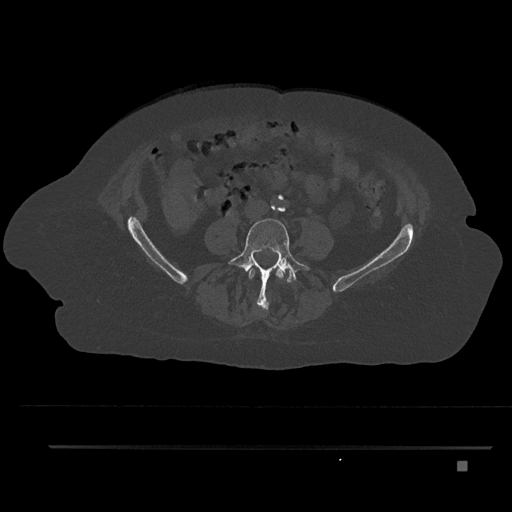
CT including the spine, one axial slice; slice 84 of 797 in the series (ordered by position); reconstruction kernel Br40s/3; 120 kVp; bone window (W 1800 / L 400 HU); 0.5 mm slice thickness; 512 × 512 image matrix, field of view 437 × 437 mm. Patient: female, 76 years. Case-level facts recorded for this patient, not image findings: primary cancer: lung; vertebrae with lytic lesions (as recorded): T11, L3.
Structures marked on this image (semi-automatic segmentation, software-assisted and operator-edited):
- L3 vertebra: bounding box <248,268,284,280> (left, top, right, bottom; pixels)
- L4 vertebra: <227,218,310,311>
- L5 vertebra: <287,270,295,282>